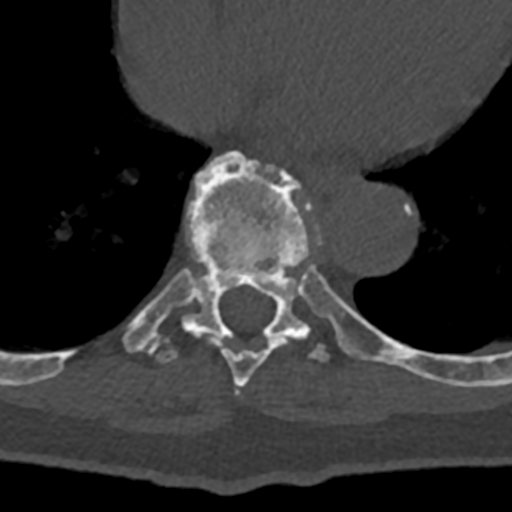
CT including the spine, one axial slice. Position 679 of 797 along the scan axis. Reconstruction kernel Br40s/3. 120 kVp. Bone window (W 1800 / L 400 HU). 0.5 mm slice thickness. 512 × 512 image matrix. Patient: male, 74 years. From the clinical record (not read from this slice): primary cancer: renal; vertebrae with lytic lesions (as recorded): T10, L1, L2, L3, L4, L5.
Annotated regions visible in this slice (semi-automatically segmented with operator editing):
- T8 vertebra: bounding box <209,279,338,387> (left, top, right, bottom; pixels)
- T9 vertebra: <122,151,432,380>